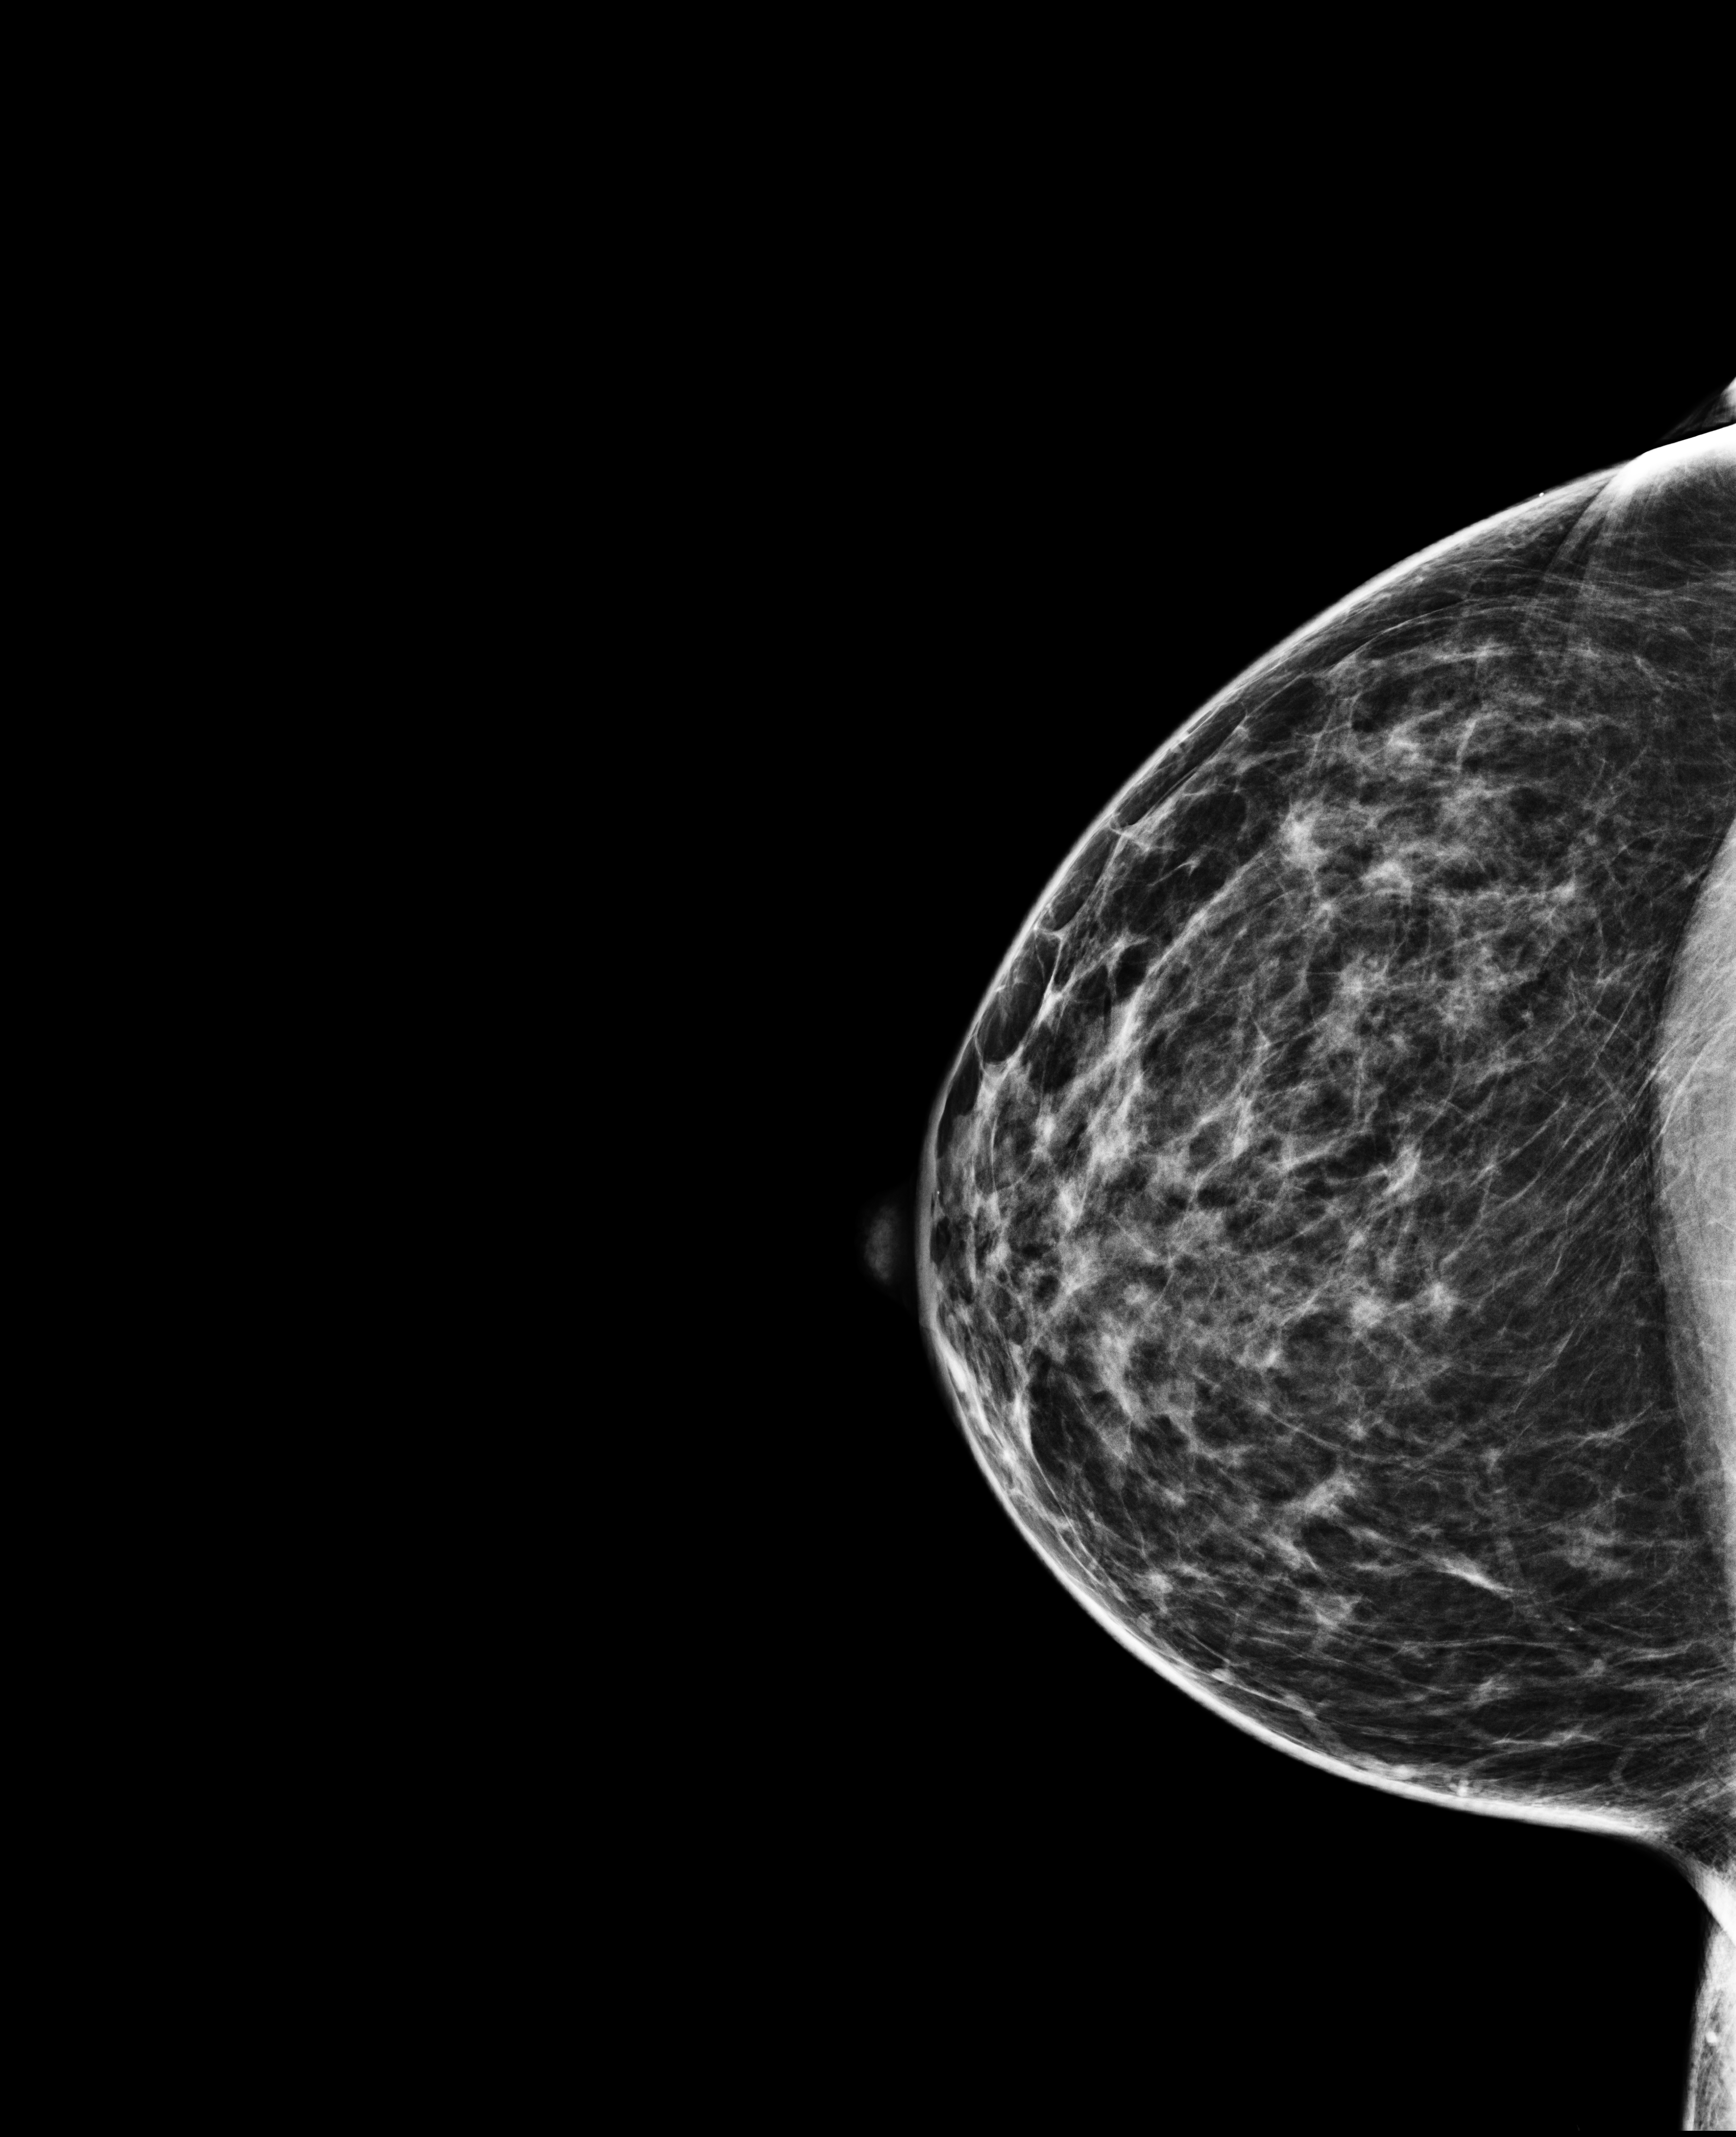
Screening examination; compressed breast thickness 61 mm; system: Selenia Dimensions. Patient: female, 49 years.
Image type: full-field digital mammogram. Breast: right. Projection: craniocaudal (CC) view.